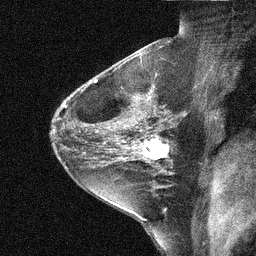
Breast MRI (dynamic contrast-enhanced), one sagittal slice; slice 28 of 44 in the series (ordered by position); dynamic contrast-enhanced study with each time point stored as its own series, time point 2 of 3 at this slice position (early post-contrast, ordered by acquisition time); 1.5 T; TE 5 ms, TR 10.3 ms; 256 × 256 image matrix. Female patient, age 31 years. Case-level facts recorded for this patient, not image findings: setting: breast cancer imaged before/during neoadjuvant chemotherapy; receptor status: HER2-positive.
Structures marked on this image (semi-automatic segmentation, software-assisted and operator-edited):
- analysis volume of interest (the breast-tissue region the enhancement analysis was run in; not a lesion): box from (x=136, y=131) to (x=181, y=168) px
- tumour enhancement mask (voxels above the 90 % enhancement threshold inside the analysis volume of interest): (x=136, y=140)–(x=172, y=162)